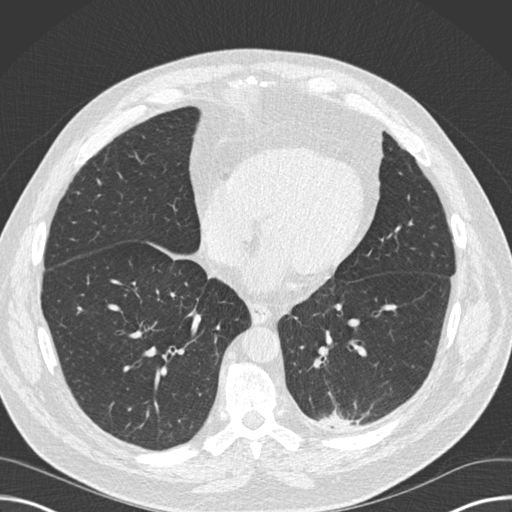
Low-dose screening chest CT, one axial slice. Position 58 of 160 along the scan axis. Reconstruction kernel B30f. 120 kVp. Lung window (W 1500 / L -600 HU). 2 mm slice thickness. 512 × 512 image matrix, field of view 382 × 382 mm.
Annotated regions visible in this slice (manually delineated by an expert):
- lesion 1 (tumor, upper lobe of left lung): bounding box (x1, y1, x2, y2) in pixels: (320, 413, 352, 426)